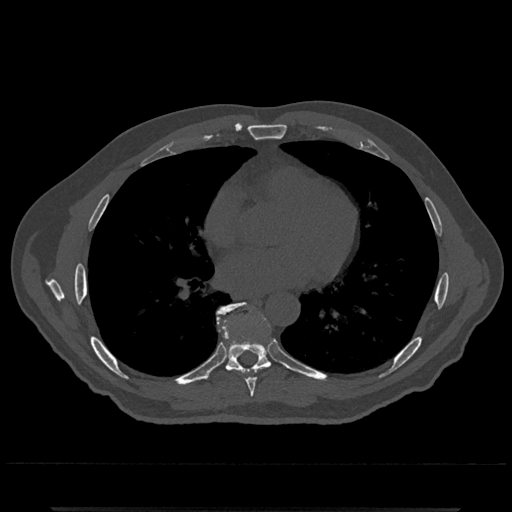
CT including the spine, one axial slice. Slice 692 of 797 in the series (ordered by position). 120 kVp. Bone window (W 1800 / L 400 HU). 0.5 mm slice thickness. 512 × 512 image matrix. Patient: male, 67 years. From the clinical record (not read from this slice): primary cancer: prostate.
Annotated regions visible in this slice (semi-automatic segmentation, software-assisted and operator-edited):
- T7 vertebra: bounding box [x1, y1, x2, y2] px = [226, 366, 271, 397]
- T8 vertebra: [216, 302, 271, 374]